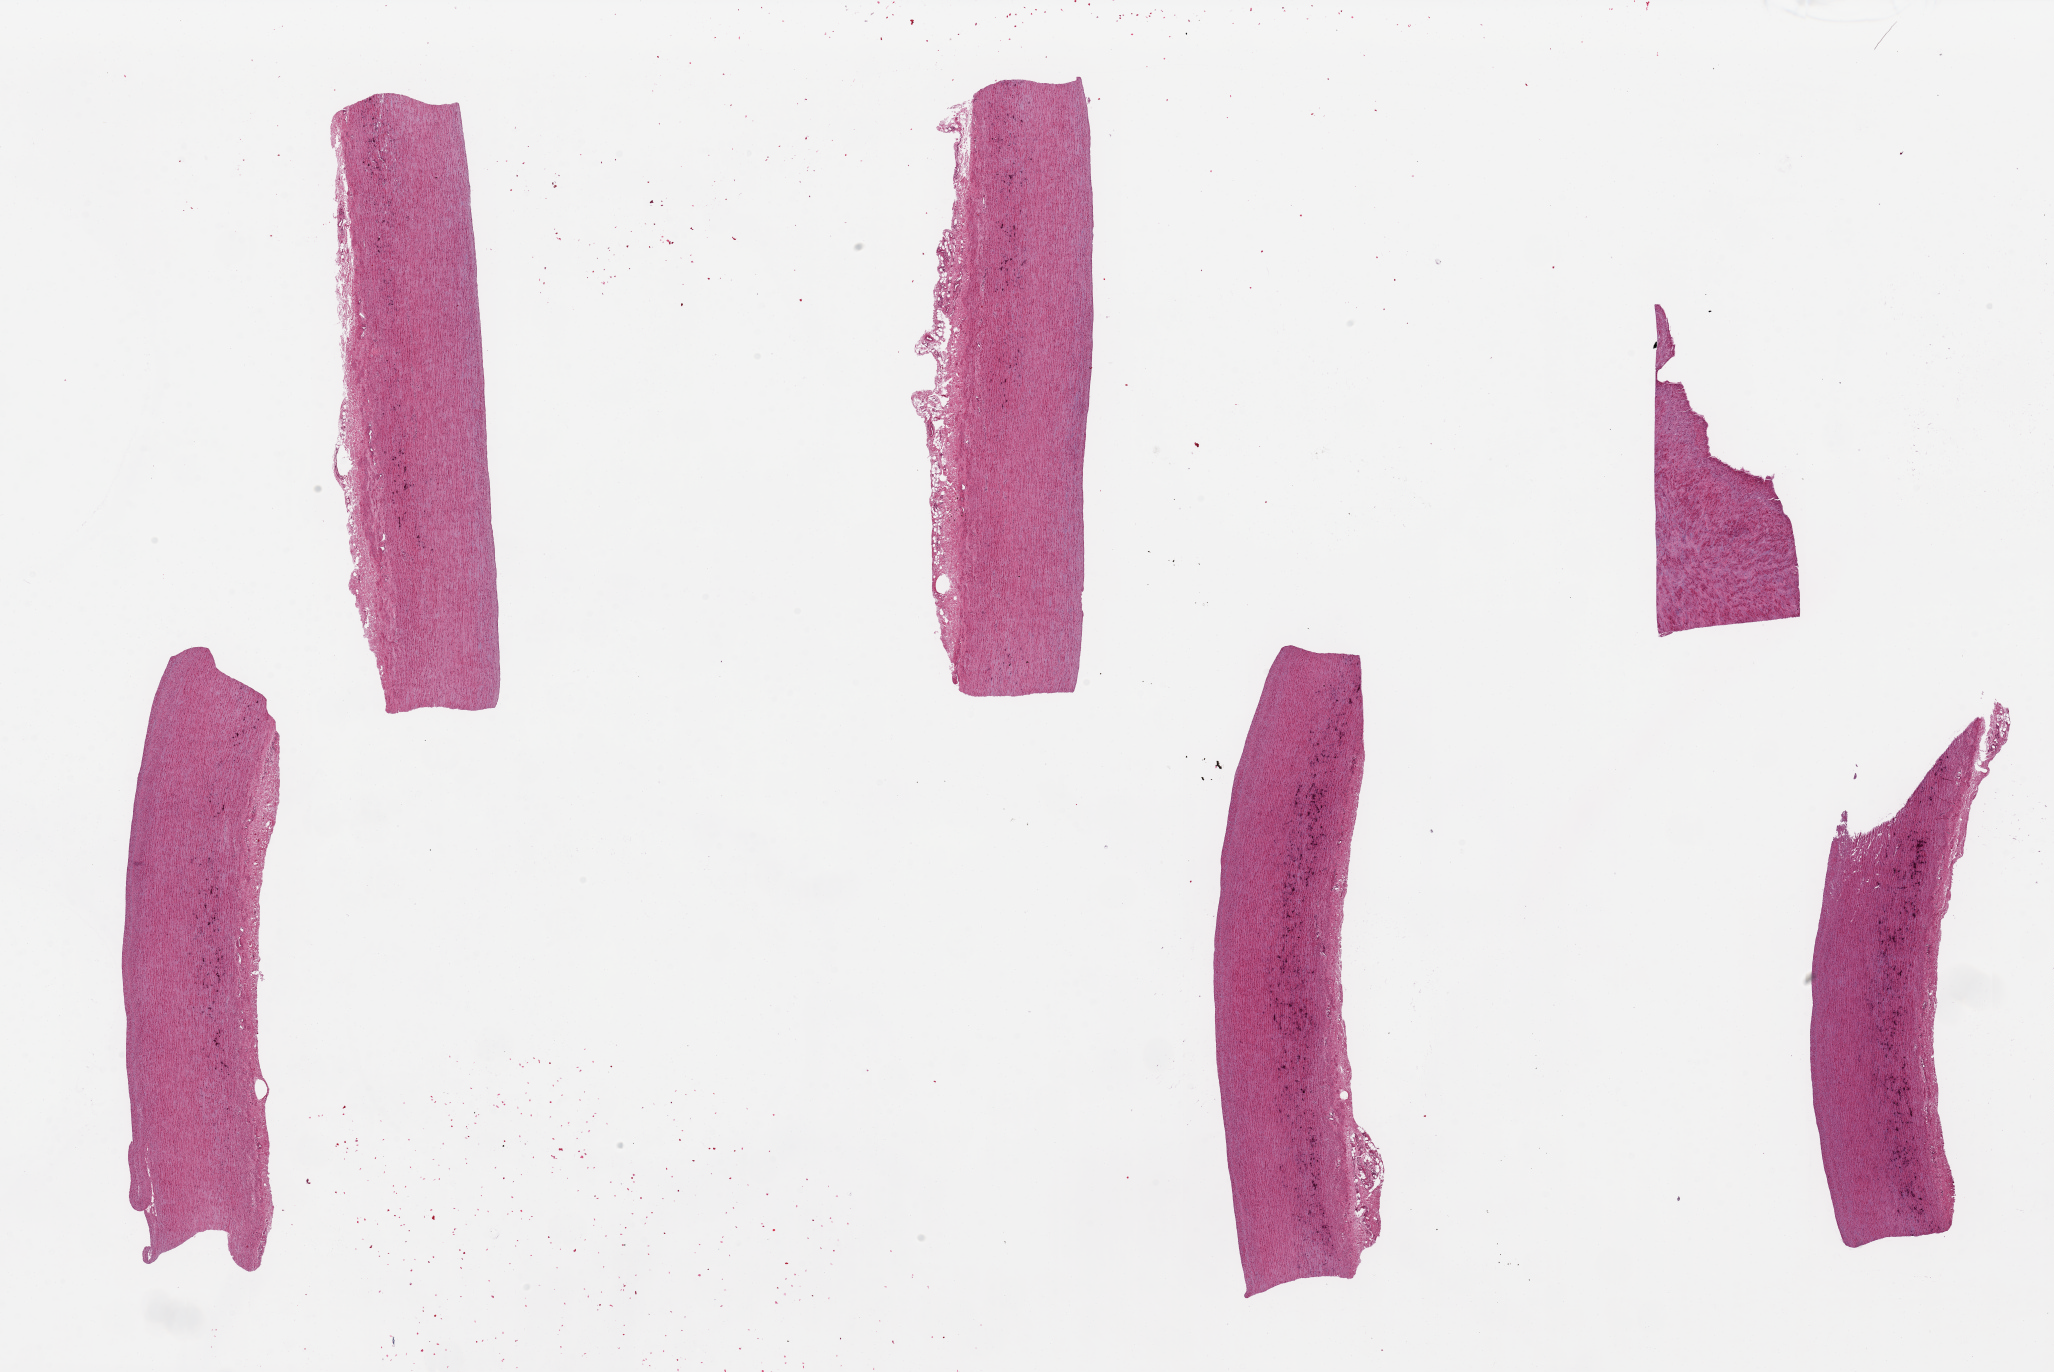
Digitized haematoxylin and eosin-stained section, whole scanned area (about 32.5 x 21.7 mm) shown as a low-resolution overview; PAXgene-fixed, paraffin-embedded tissue; sampled site (target tissue): aorta; tissue donor sample. Donor sex: male.
Pathologist's review note for this sample: 6 pieces, up to 10x2.5mm; well trimmed, no plaques.